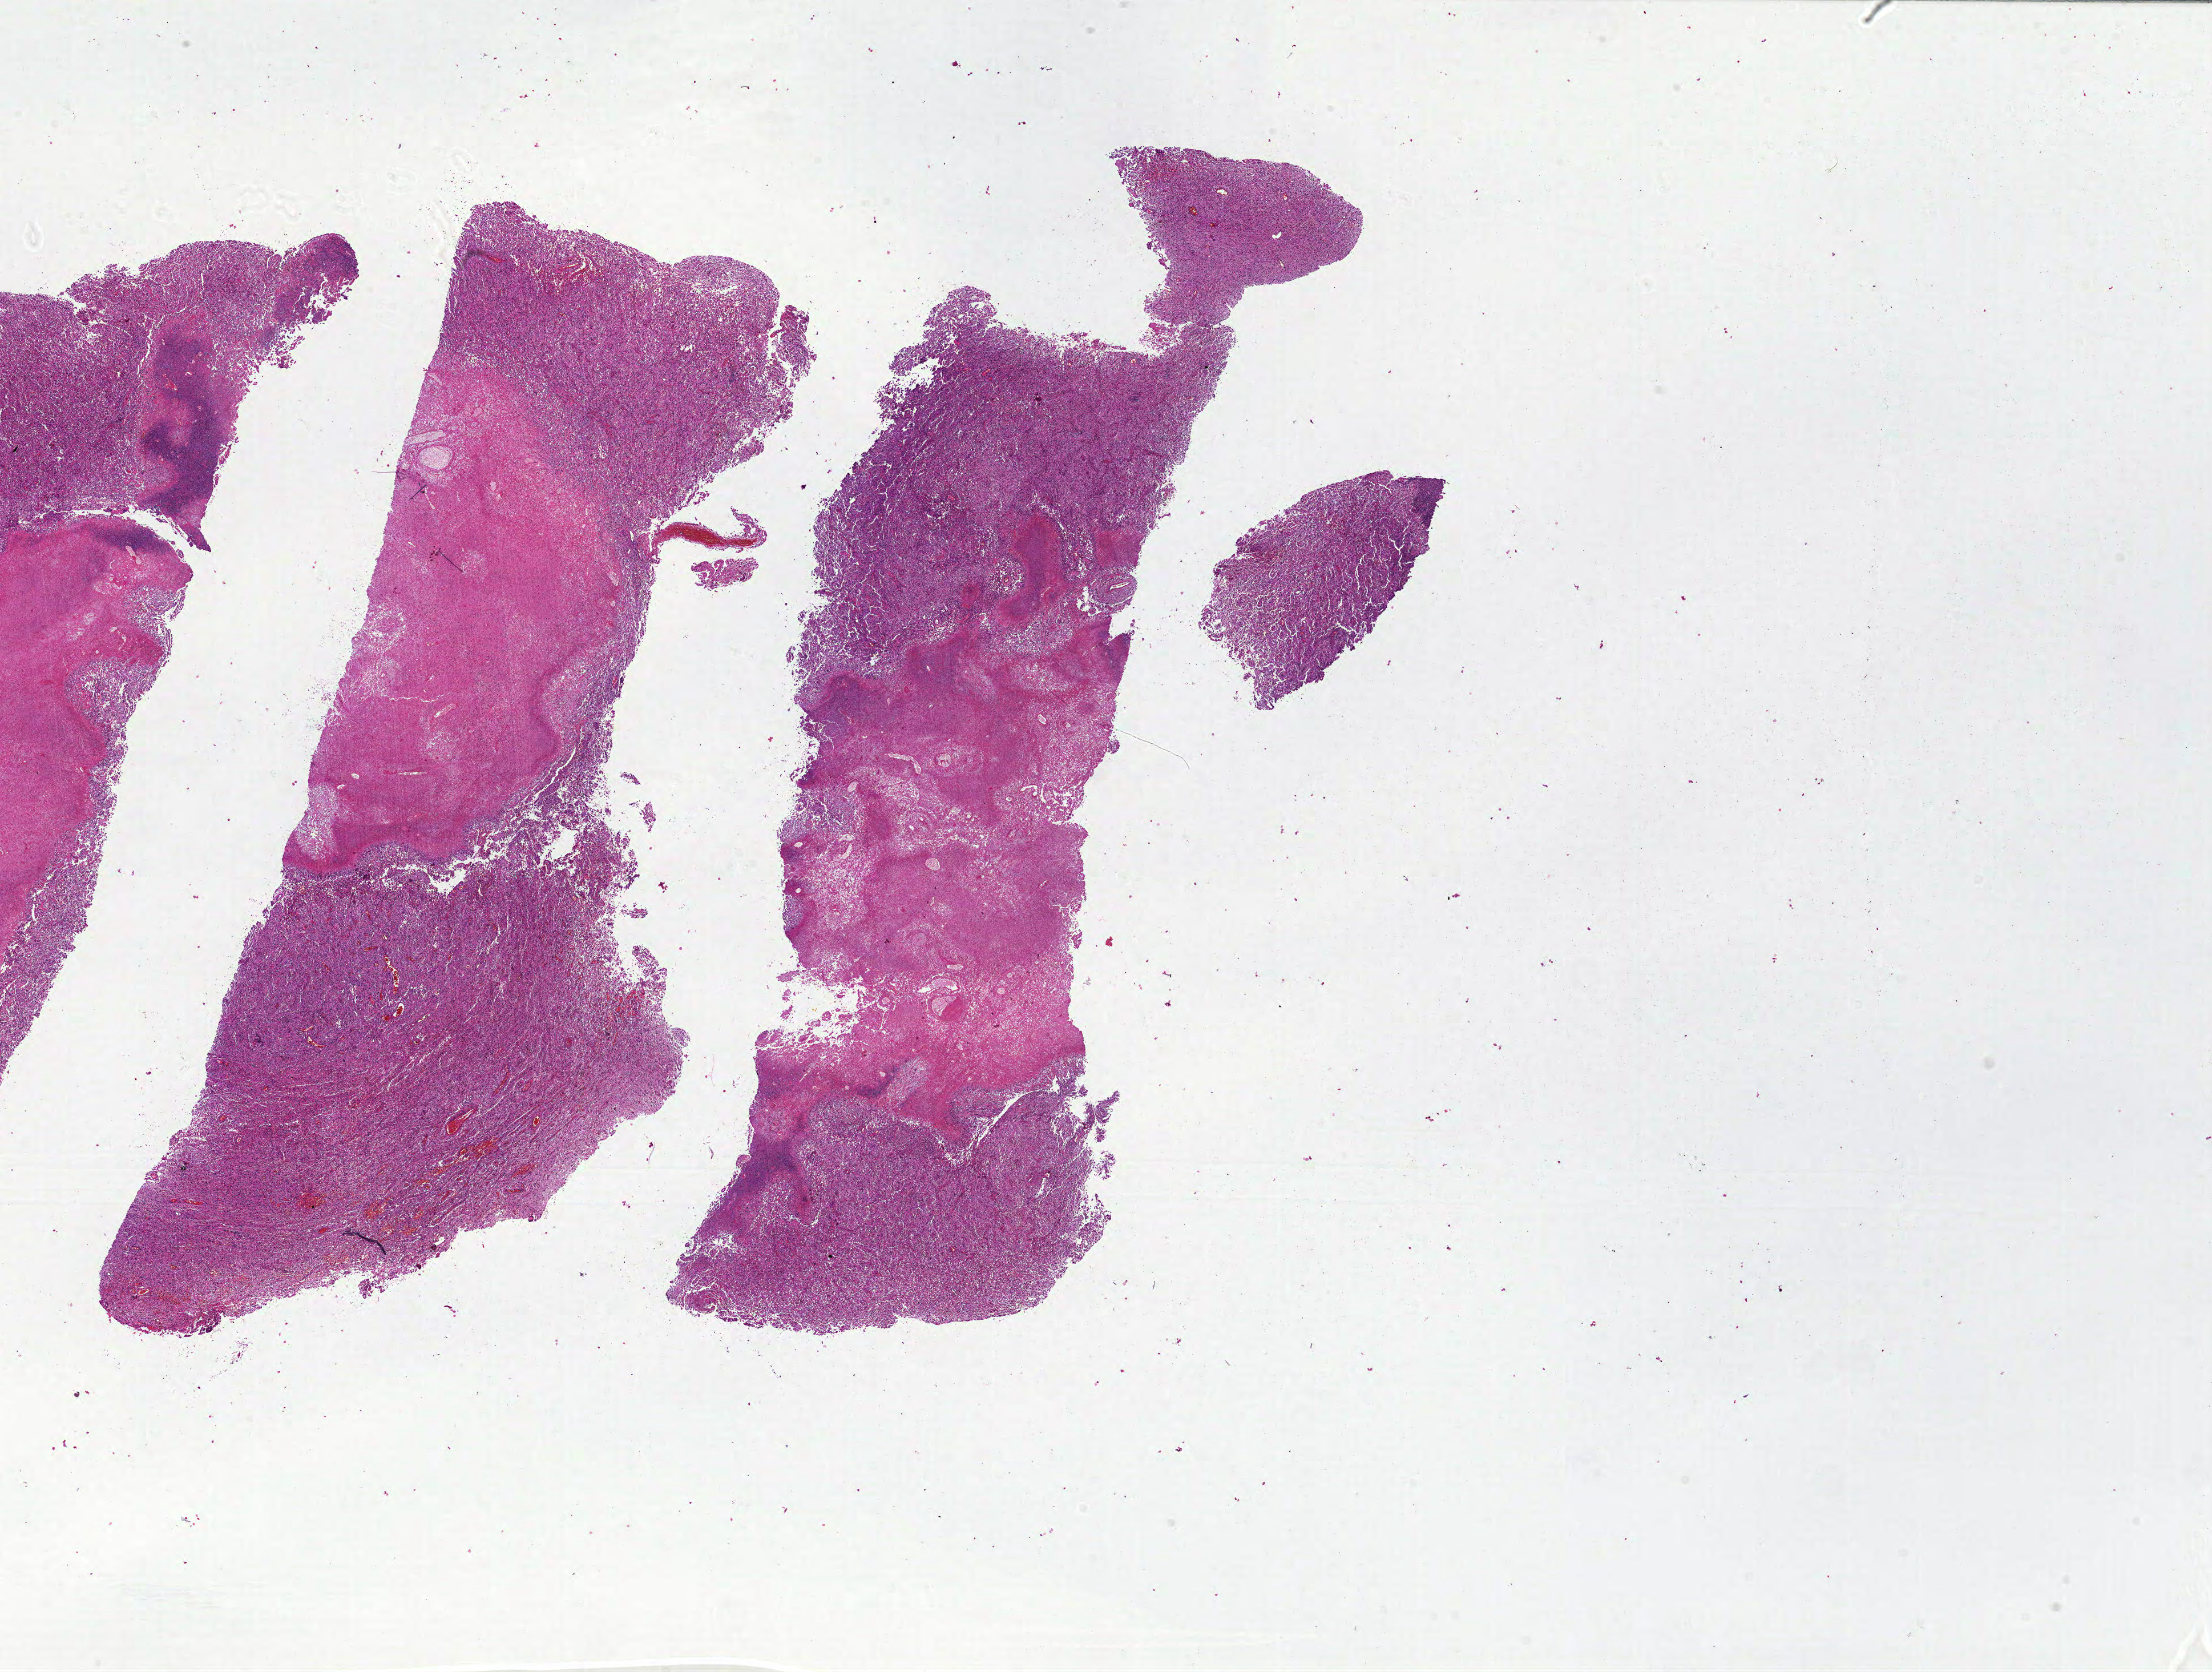
Whole-slide histology image, H&E-stained — low-resolution overview of the scanned area, about 31.0 x 23.4 mm (slide scanned at 20x). FFPE section. Brain, primary tumour sample. Male, age 46 years at initial diagnosis.
Diagnosis: Glioblastoma.